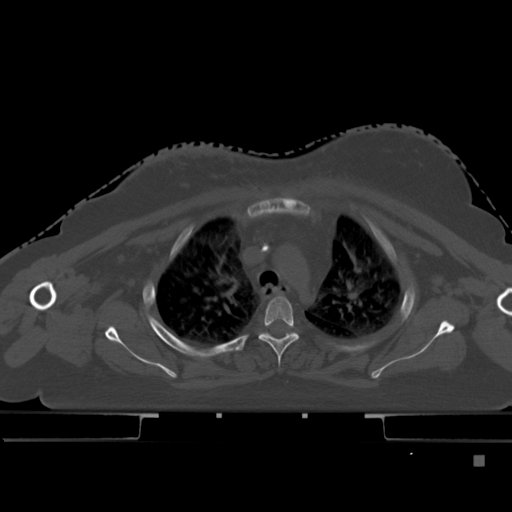
CT including the spine, one axial slice. Position 344 of 495 along the scan axis. Bone window (W 1800 / L 400 HU). 512 × 512 image matrix, field of view 404 × 404 mm. Patient: female, 33 years. From the clinical record (not read from this slice): primary cancer: breast; vertebrae with lytic lesions (as recorded): T1.
Outlined on this slice (semi-automatically segmented with operator editing):
- T3 vertebra: bounding box (x1, y1, x2, y2) in pixels: (259, 295, 299, 368)
- T4 vertebra: (260, 332, 298, 335)